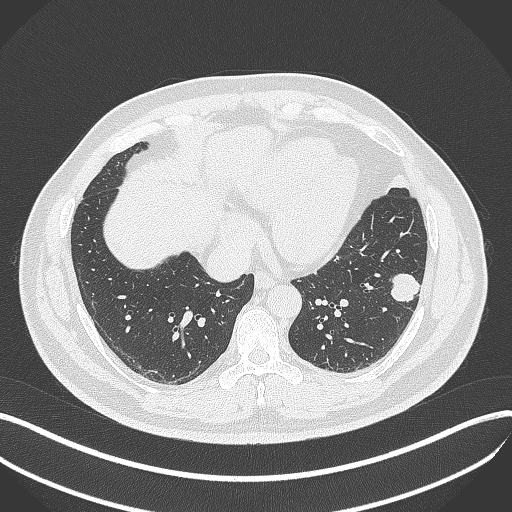
Chest CT, one axial slice; slice 141 of 429 in the series (ordered by position); reconstruction kernel B70f; 120 kVp; lung window (W 1500 / L -600 HU); 1 mm slice thickness; 512 × 512 image matrix. Patient: male, 39 years. From the clinical record (not read from this slice): clinical TNM (as recorded): T2a N0 M0; histopathological grade: G2-3.
Annotated regions visible in this slice (bounding box drawn by a radiologist):
- lung tumour (recorded histology: adenocarcinoma): bounding box (x1, y1, x2, y2) in pixels: (385, 271, 423, 306)